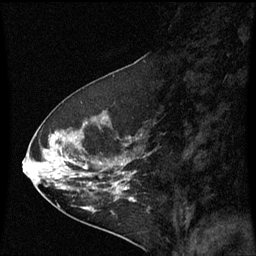
Breast MRI (dynamic contrast-enhanced), one sagittal slice; slice 26 of 60 in the series (ordered by position); dynamic contrast-enhanced series, image 2 of 3 at this slice position (ordered by acquisition); 1.5 T; TE 4.2 ms, TR 8.9 ms; 2 mm slice thickness; 256 × 256 image matrix, field of view 200 × 200 mm. Patient: female, 53 years. From the clinical record (not read from this slice): setting: breast cancer imaged before/during neoadjuvant chemotherapy; receptor status: HR-positive, HER2-negative.
Outlined on this slice (semi-automatic segmentation, software-assisted and operator-edited):
- analysis volume of interest (the breast-tissue region the enhancement analysis was run in; not a lesion): bounding box [x1, y1, x2, y2] px = [32, 100, 145, 221]
- tumour enhancement mask (voxels above the 70 % enhancement threshold inside the analysis volume of interest): [52, 134, 133, 211]